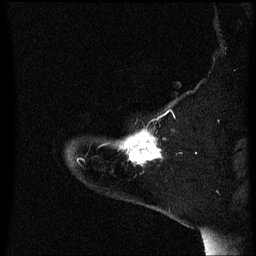
Breast MRI (dynamic contrast-enhanced), one sagittal slice; slice 51 of 60 in the series (ordered by position); dynamic contrast-enhanced series, image 2 of 3 at this slice position (ordered by acquisition); 1.5 T; TE 4.2 ms, TR 8.4 ms; 2 mm slice thickness; 256 × 256 image matrix. Patient: female, 54 years. From the clinical record (not read from this slice): setting: breast cancer imaged before/during neoadjuvant chemotherapy; receptor status: HR-positive, HER2-negative.
Structures marked on this image (semi-automatic segmentation, software-assisted and operator-edited):
- analysis volume of interest (the breast-tissue region the enhancement analysis was run in; not a lesion): bounding box <118,130,164,167> (left, top, right, bottom; pixels)
- tumour enhancement mask (voxels above the 70 % enhancement threshold inside the analysis volume of interest): <125,130,163,165>